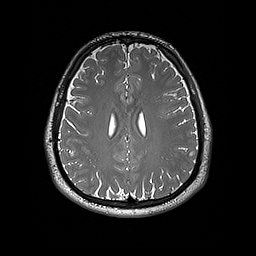
Brain MRI from a brain-tumour surgery series, one axial slice; position 73 of 192 along the scan axis; 256 × 256 image matrix. From the clinical record (not read from this slice): histopathology: Dysembryoplastic neuroepithelial tumor; WHO grade: 1; IDH mutation: no; tumour location: Left Inferior Parietal.
Annotated regions visible in this slice (expert manual segmentation):
- tumour: box from (x=189, y=149) to (x=197, y=156) px